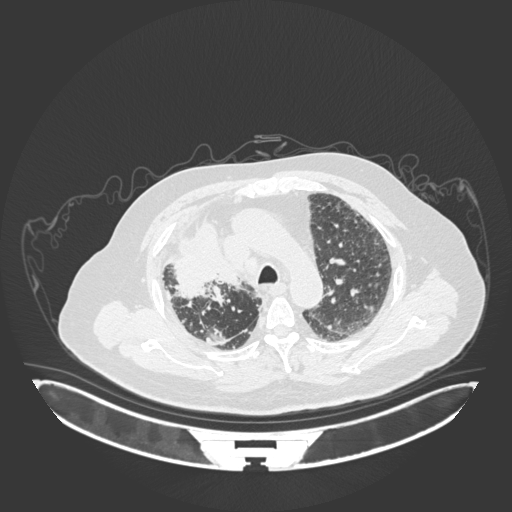
Chest CT, one axial slice. Slice 132 of 201 in the series (ordered by position). Reconstruction kernel B30f. 120 kVp. Lung window (W 1500 / L -600 HU). 512 × 512 image matrix. Patient: male, 69 years. From the clinical record (not read from this slice): clinical TNM (as recorded): T4 N3 M1.
Annotated regions visible in this slice (bounding box drawn by a radiologist):
- lung tumour (recorded histology: adenocarcinoma): bounding box (x1, y1, x2, y2) in pixels: (162, 220, 237, 299)